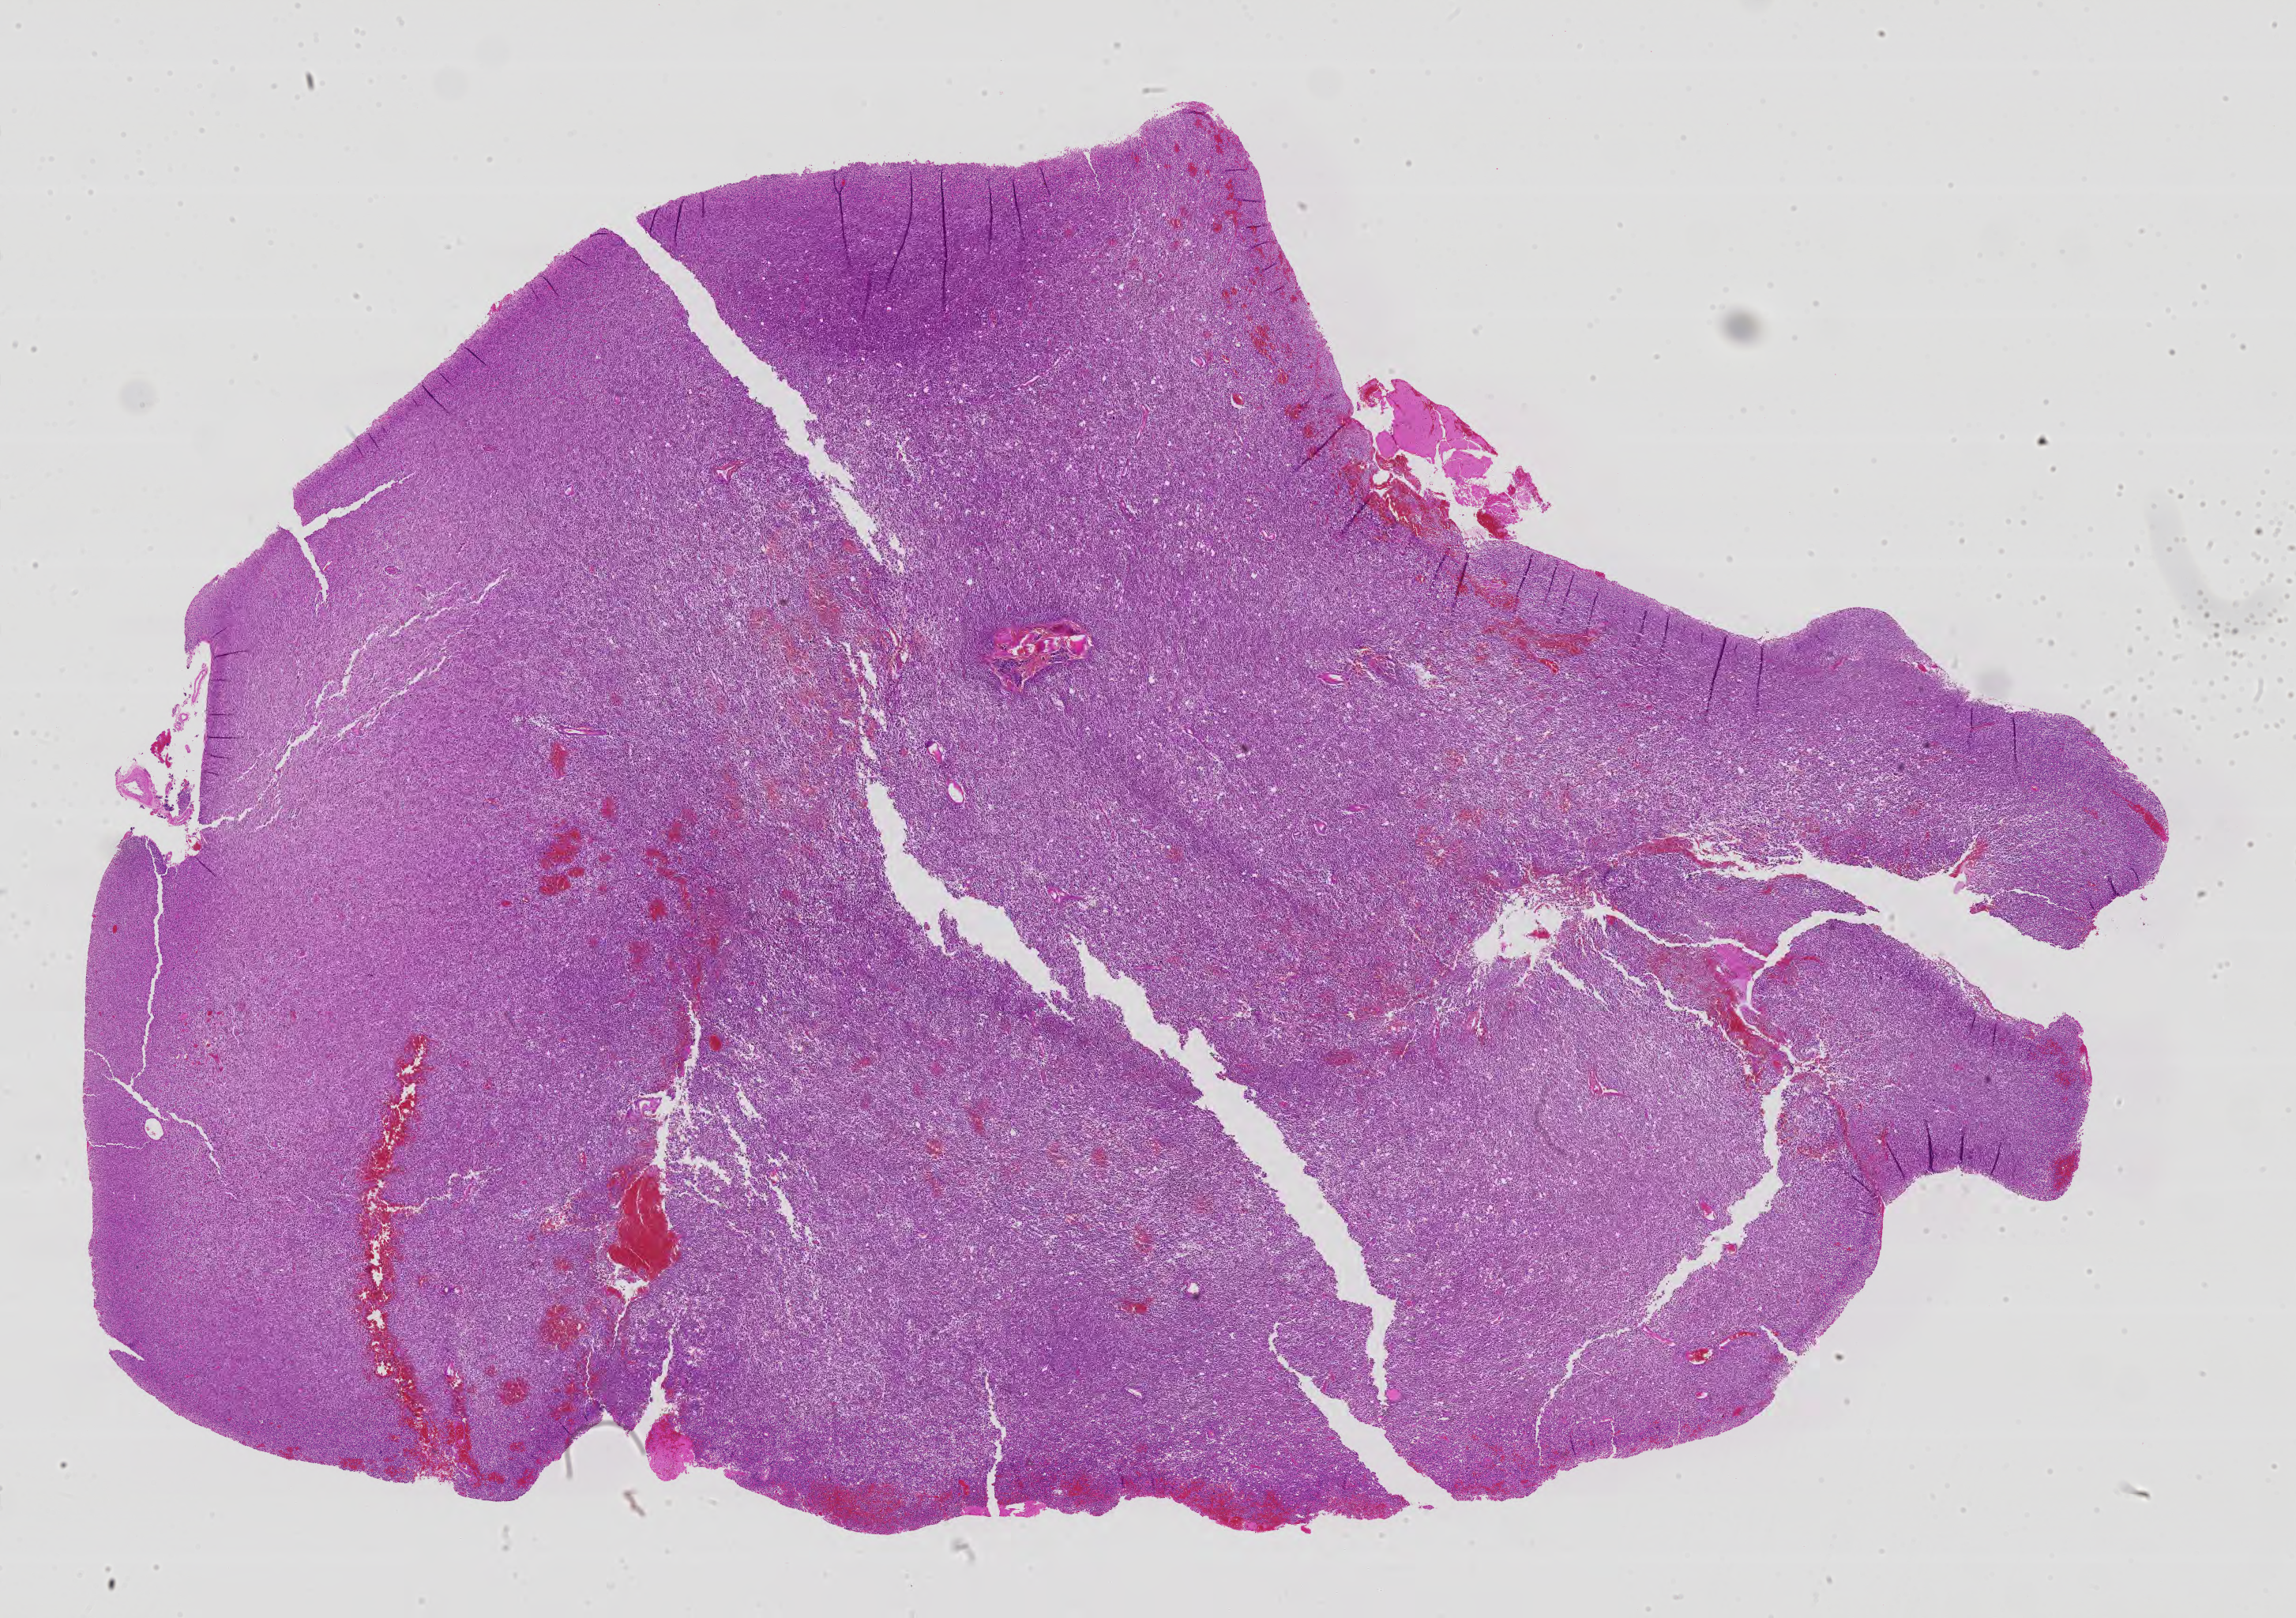
H&E-stained whole-slide image — low-resolution overview of the scanned area, about 23.3 x 16.4 mm, FFPE section, brain, primary tumour sample. Female, age 33 years at initial diagnosis.
Histologic diagnosis: Astrocytoma, anaplastic (cerebrum).